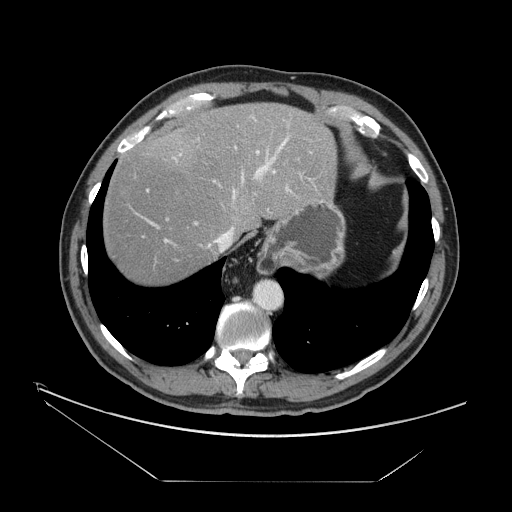
Contrast-enhanced abdominal CT, one axial slice. Position 130 of 161 along the scan axis. 120 kVp. Intravenous contrast given. Soft-tissue window (W 400 / L 40 HU). 2.5 mm slice thickness. 512 × 512 image matrix. Male patient, age 65 years. From the clinical record (not read from this slice): diagnosis: colorectal cancer liver metastases, imaged before liver resection; multiple liver metastases: yes; largest metastasis: 4.2 cm; disease in both lobes: yes.
Annotated regions visible in this slice (manually delineated by an expert):
- hepatic veins: box from (x=206, y=126) to (x=288, y=253) px
- liver: (x=103, y=103)–(x=335, y=285)
- planned liver remnant (the part of the liver to remain after resection): (x=102, y=103)–(x=336, y=285)
- portal vein (with intrahepatic branches): (x=146, y=115)–(x=291, y=243)